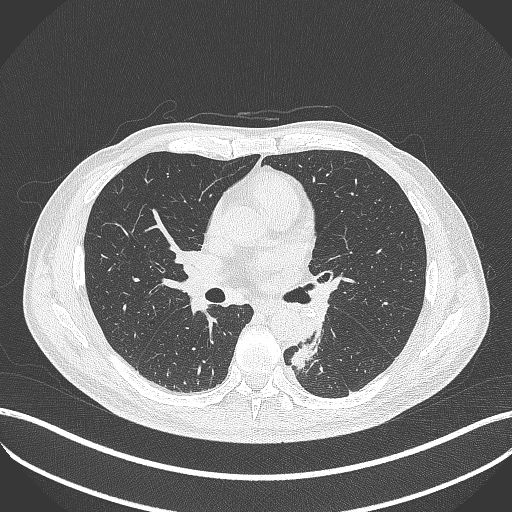
Chest CT, one axial slice. Lung window (W 1500 / L -600 HU). 512 × 512 image matrix, field of view 400 × 400 mm. Male patient, age 72 years. Case-level facts recorded for this patient, not image findings: clinical TNM (as recorded): T2b N0 M1.
Structures marked on this image (rectangle marked by the reading radiologist):
- lung tumour (recorded histology: adenocarcinoma): bounding box (x1, y1, x2, y2) in pixels: (285, 326, 327, 369)